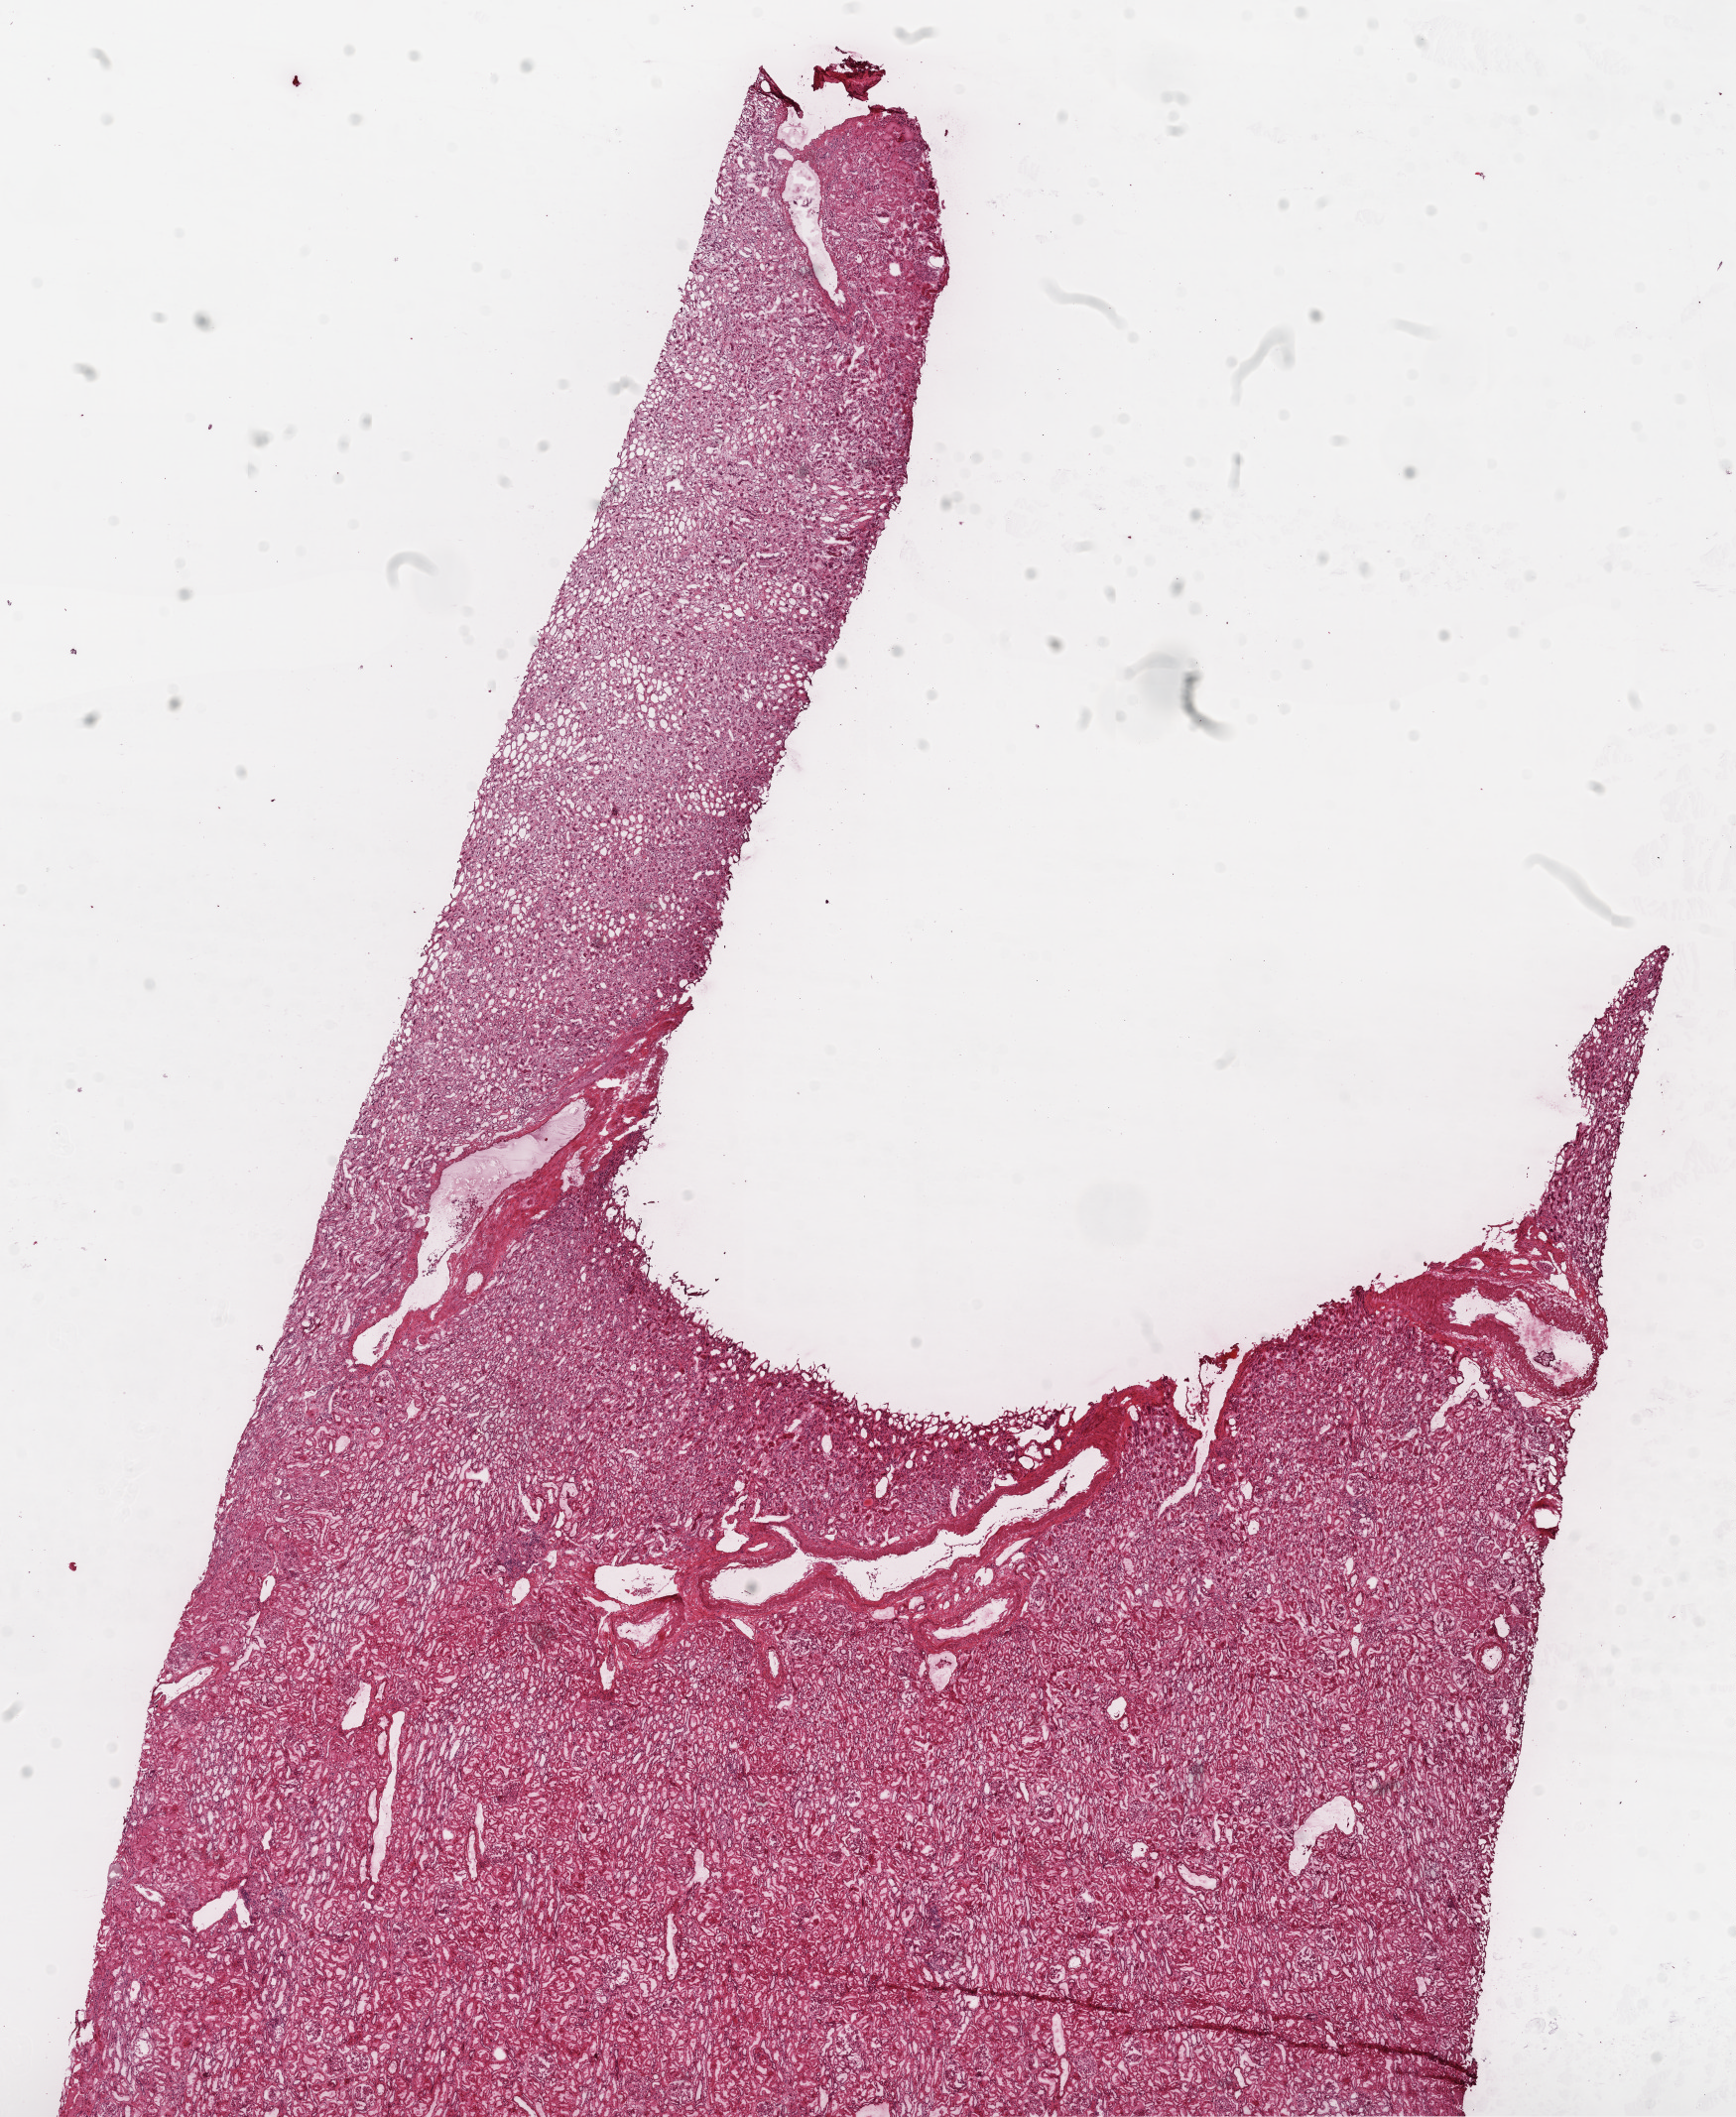
Hematoxylin and eosin (H&E) stained whole-slide image — a low-resolution overview of the entire scanned area, about 14.0 x 17.1 mm, frozen section, sample: solid tissue normal (non-tumour tissue), kidney. Female, age 59 years at initial diagnosis.
- this section: solid tissue normal sample (biorepository sample class)
- patient diagnosis: Clear cell adenocarcinoma, NOS